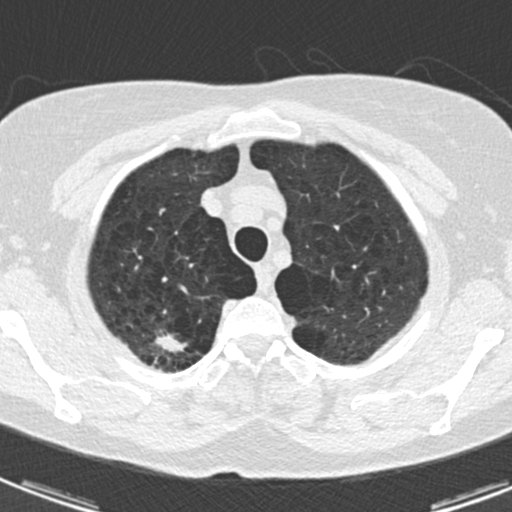
Axial slice from a low-dose chest CT screening exam; third annual screen; lung window (W 1500 / L -600 HU); 2 mm slice thickness; 120 kVp; slice 24 of 174 in the series; 512 × 512 image matrix. Female participant, aged 59 years at enrolment.
• Expert reader's lesion annotation, bounding box <133,320,192,366> (left, top, right, bottom; pixels).
• Screening reader's record for this exam (one nodule recorded; not confirmed to be the boxed lesion): non-calcified nodule or mass ≥4 mm, right upper lobe, 12 × 7 mm, spiculated (stellate) margins, soft tissue attenuation, pre-existing on the prior screen: yes; interval growth: yes.
• Later outcome: lung cancer diagnosed 32 days after this screen — adenocarcinoma, NOS, right upper lobe, poorly differentiated (G3), stage IA (AJCC 6th edition), 20 mm at pathology.